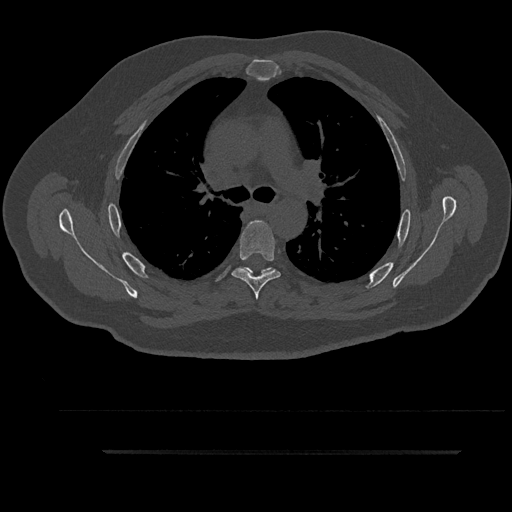
CT including the spine, one axial slice. Slice 624 of 797 in the series (ordered by position). Reconstruction kernel Br40s/3. 120 kVp. Bone window (W 1800 / L 400 HU). 0.5 mm slice thickness. 512 × 512 image matrix, field of view 432 × 432 mm. Male patient, age 63 years. Case-level facts recorded for this patient, not image findings: primary cancer: renal; vertebrae with lytic lesions (as recorded): T8.
Annotated regions visible in this slice (semi-automatic segmentation, software-assisted and operator-edited):
- T5 vertebra: box from (x=231, y=221) to (x=281, y=300) px
- T6 vertebra: (x=244, y=268)–(x=275, y=277)